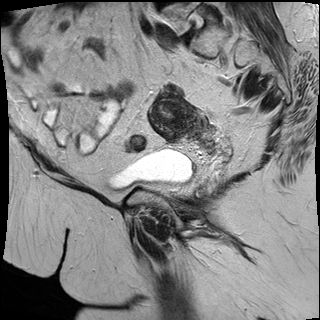
Pelvic MRI for cervical cancer, one sagittal slice. Slice 13 of 32 in the series (ordered by position). T2-weighted. 1.5 T. TE 87 ms, TR 3063.4 ms. 4 mm slice thickness. 320 × 320 image matrix, field of view 280 × 280 mm. Patient: female, 53 years.
Annotated regions visible in this slice (outlined manually by an expert reader):
- uterus and cervix: bounding box [x1, y1, x2, y2] px = [148, 94, 208, 142]